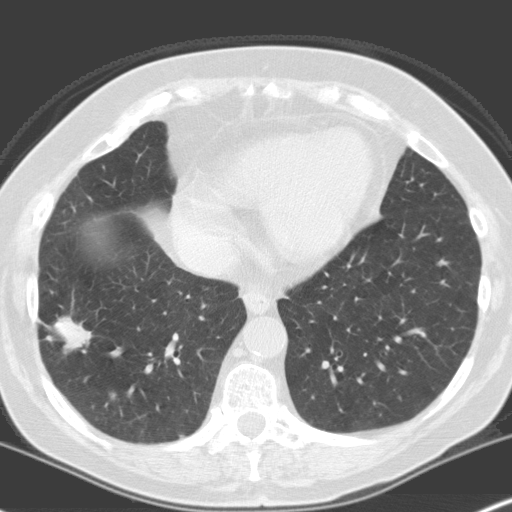
Low-dose screening chest CT, one axial slice. Slice 62 of 160 in the series (ordered by position). Lung window (W 1500 / L -600 HU). 512 × 512 image matrix.
Outlined on this slice (manually delineated by an expert):
- lesion 1 (tumor, lower lobe of right lung): bounding box <48,315,92,352> (left, top, right, bottom; pixels)